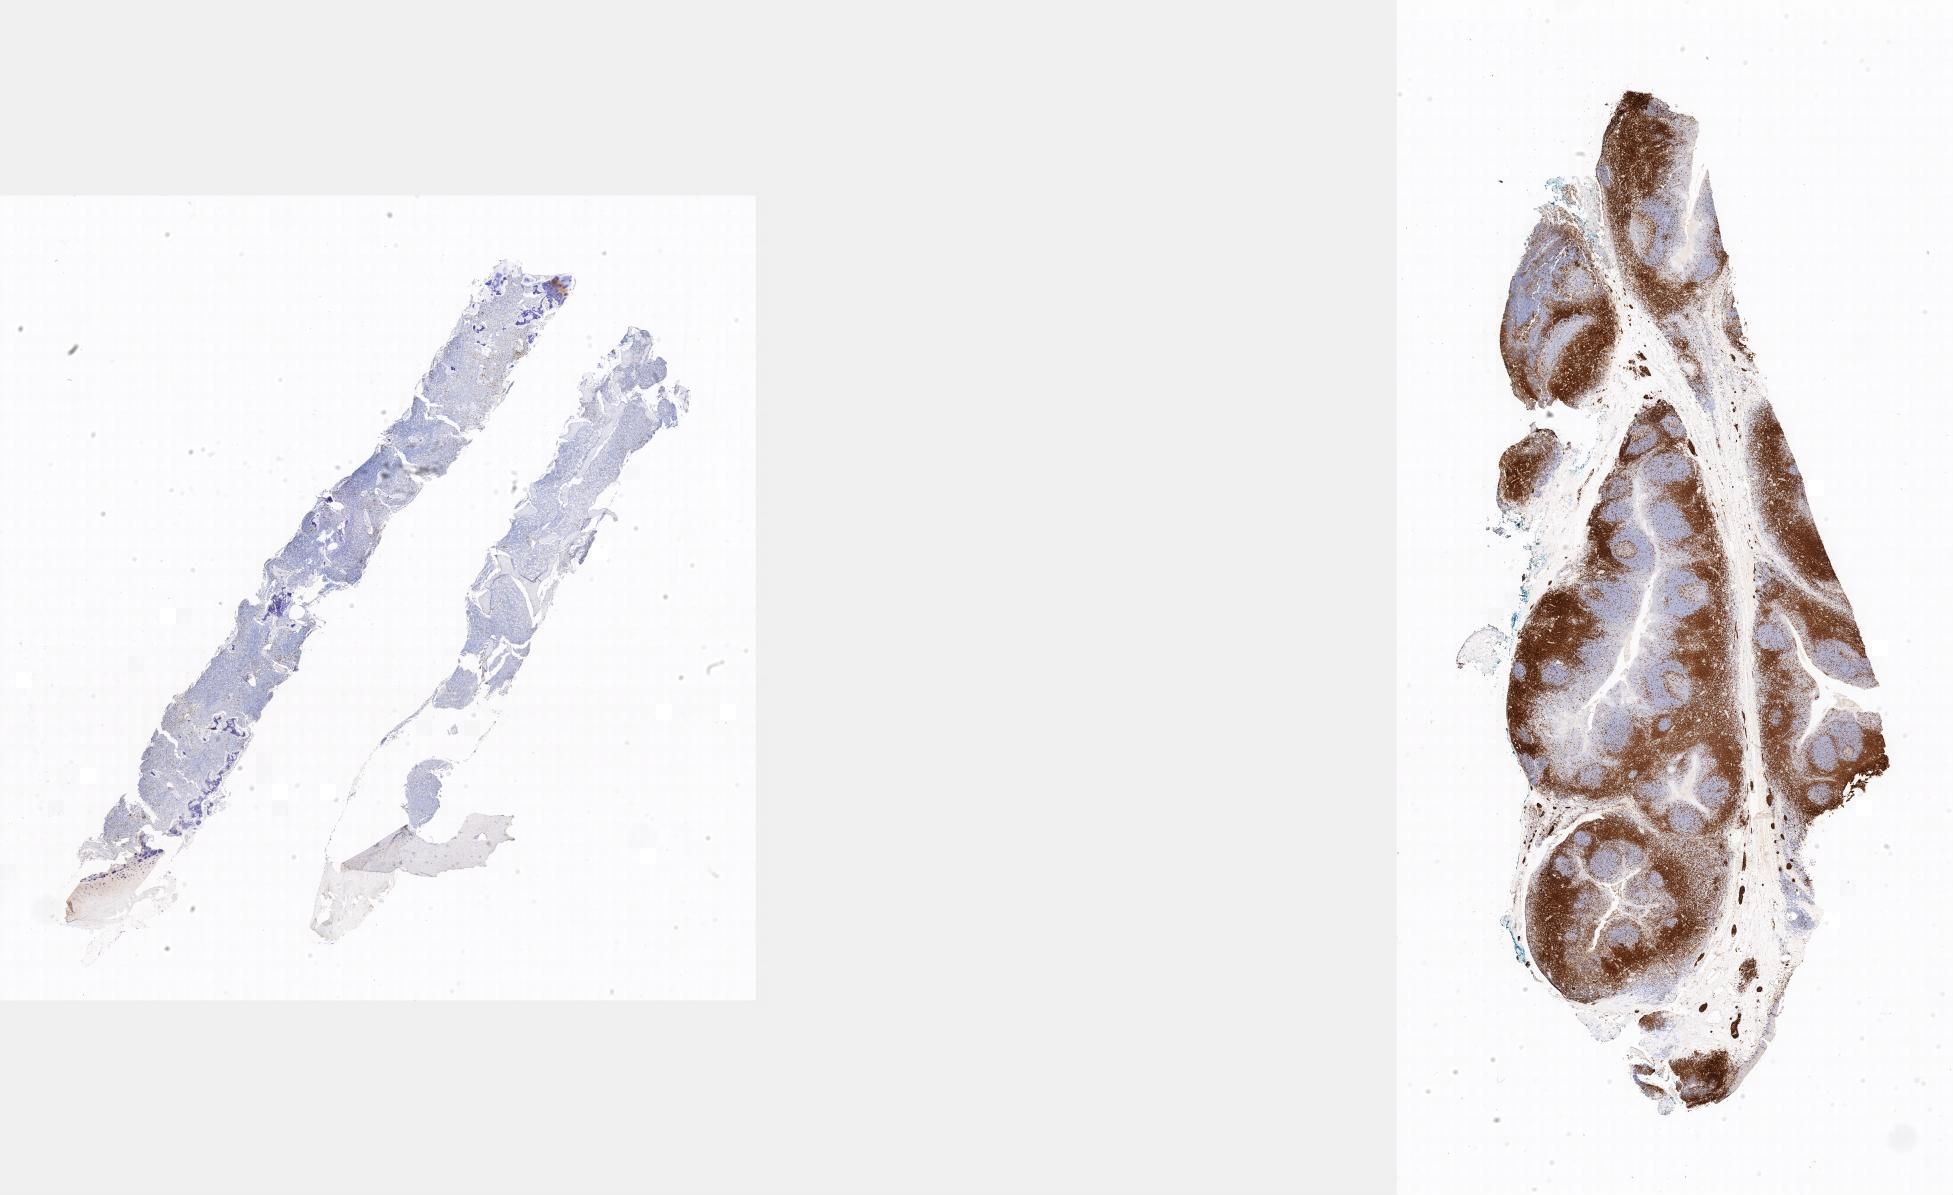
Whole-slide image, immunohistochemical stain for CD3 — shown as a low-resolution overview of the whole scanned area; tumor tissue; site: bone marrow. Patient male; aged 16.
Histologic diagnosis: Burkitt lymphoma, NOS.